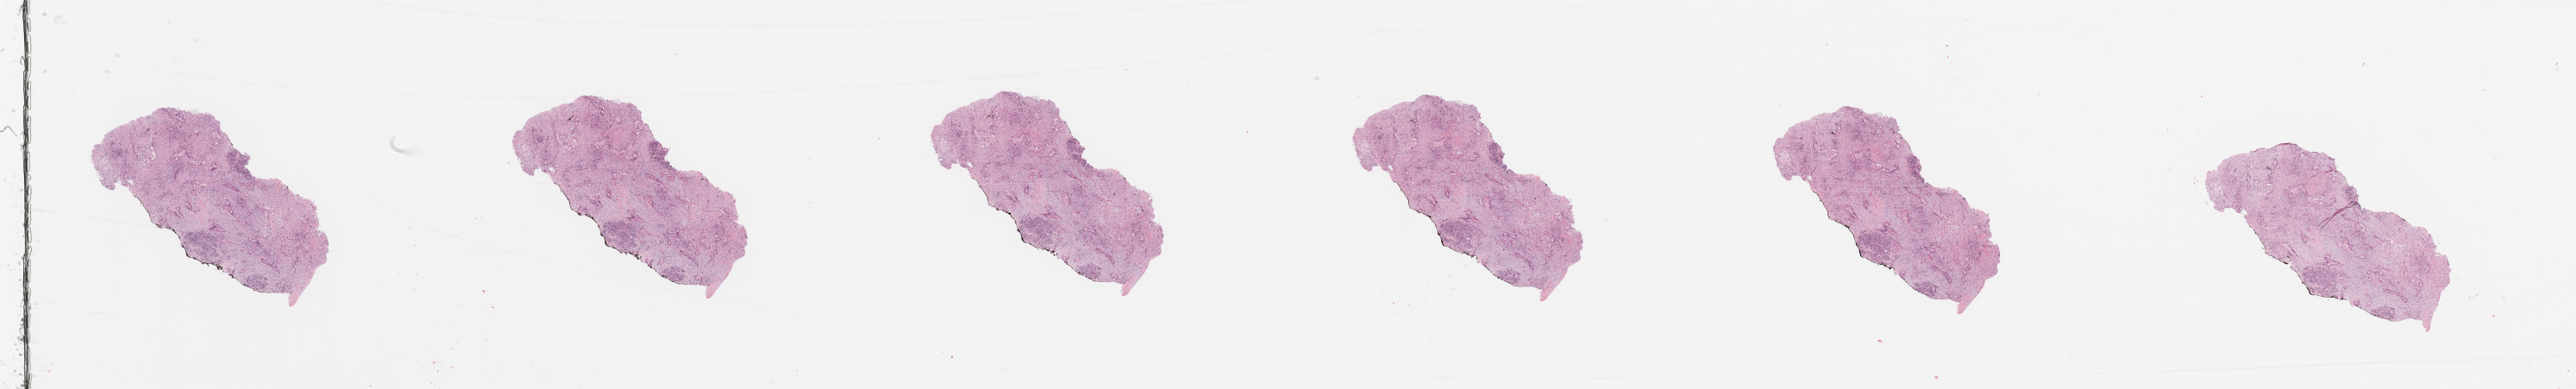
Whole-slide histology image, Hematoxylin and eosin (H&E) stained, a low-resolution overview of the entire scanned area, about 47.3 x 7.1 mm (acquisition: 20x scan); tumour tissue sample, sampled site: pancreas. Patient: female, age 69 years. Histologic grade: G2 (moderately differentiated). Composition of this section per pathologist review: tumour nuclei 30%, necrosis 0%.
* AJCC pathologic stage: IIB
* diagnosis: Infiltrating duct carcinoma, NOS